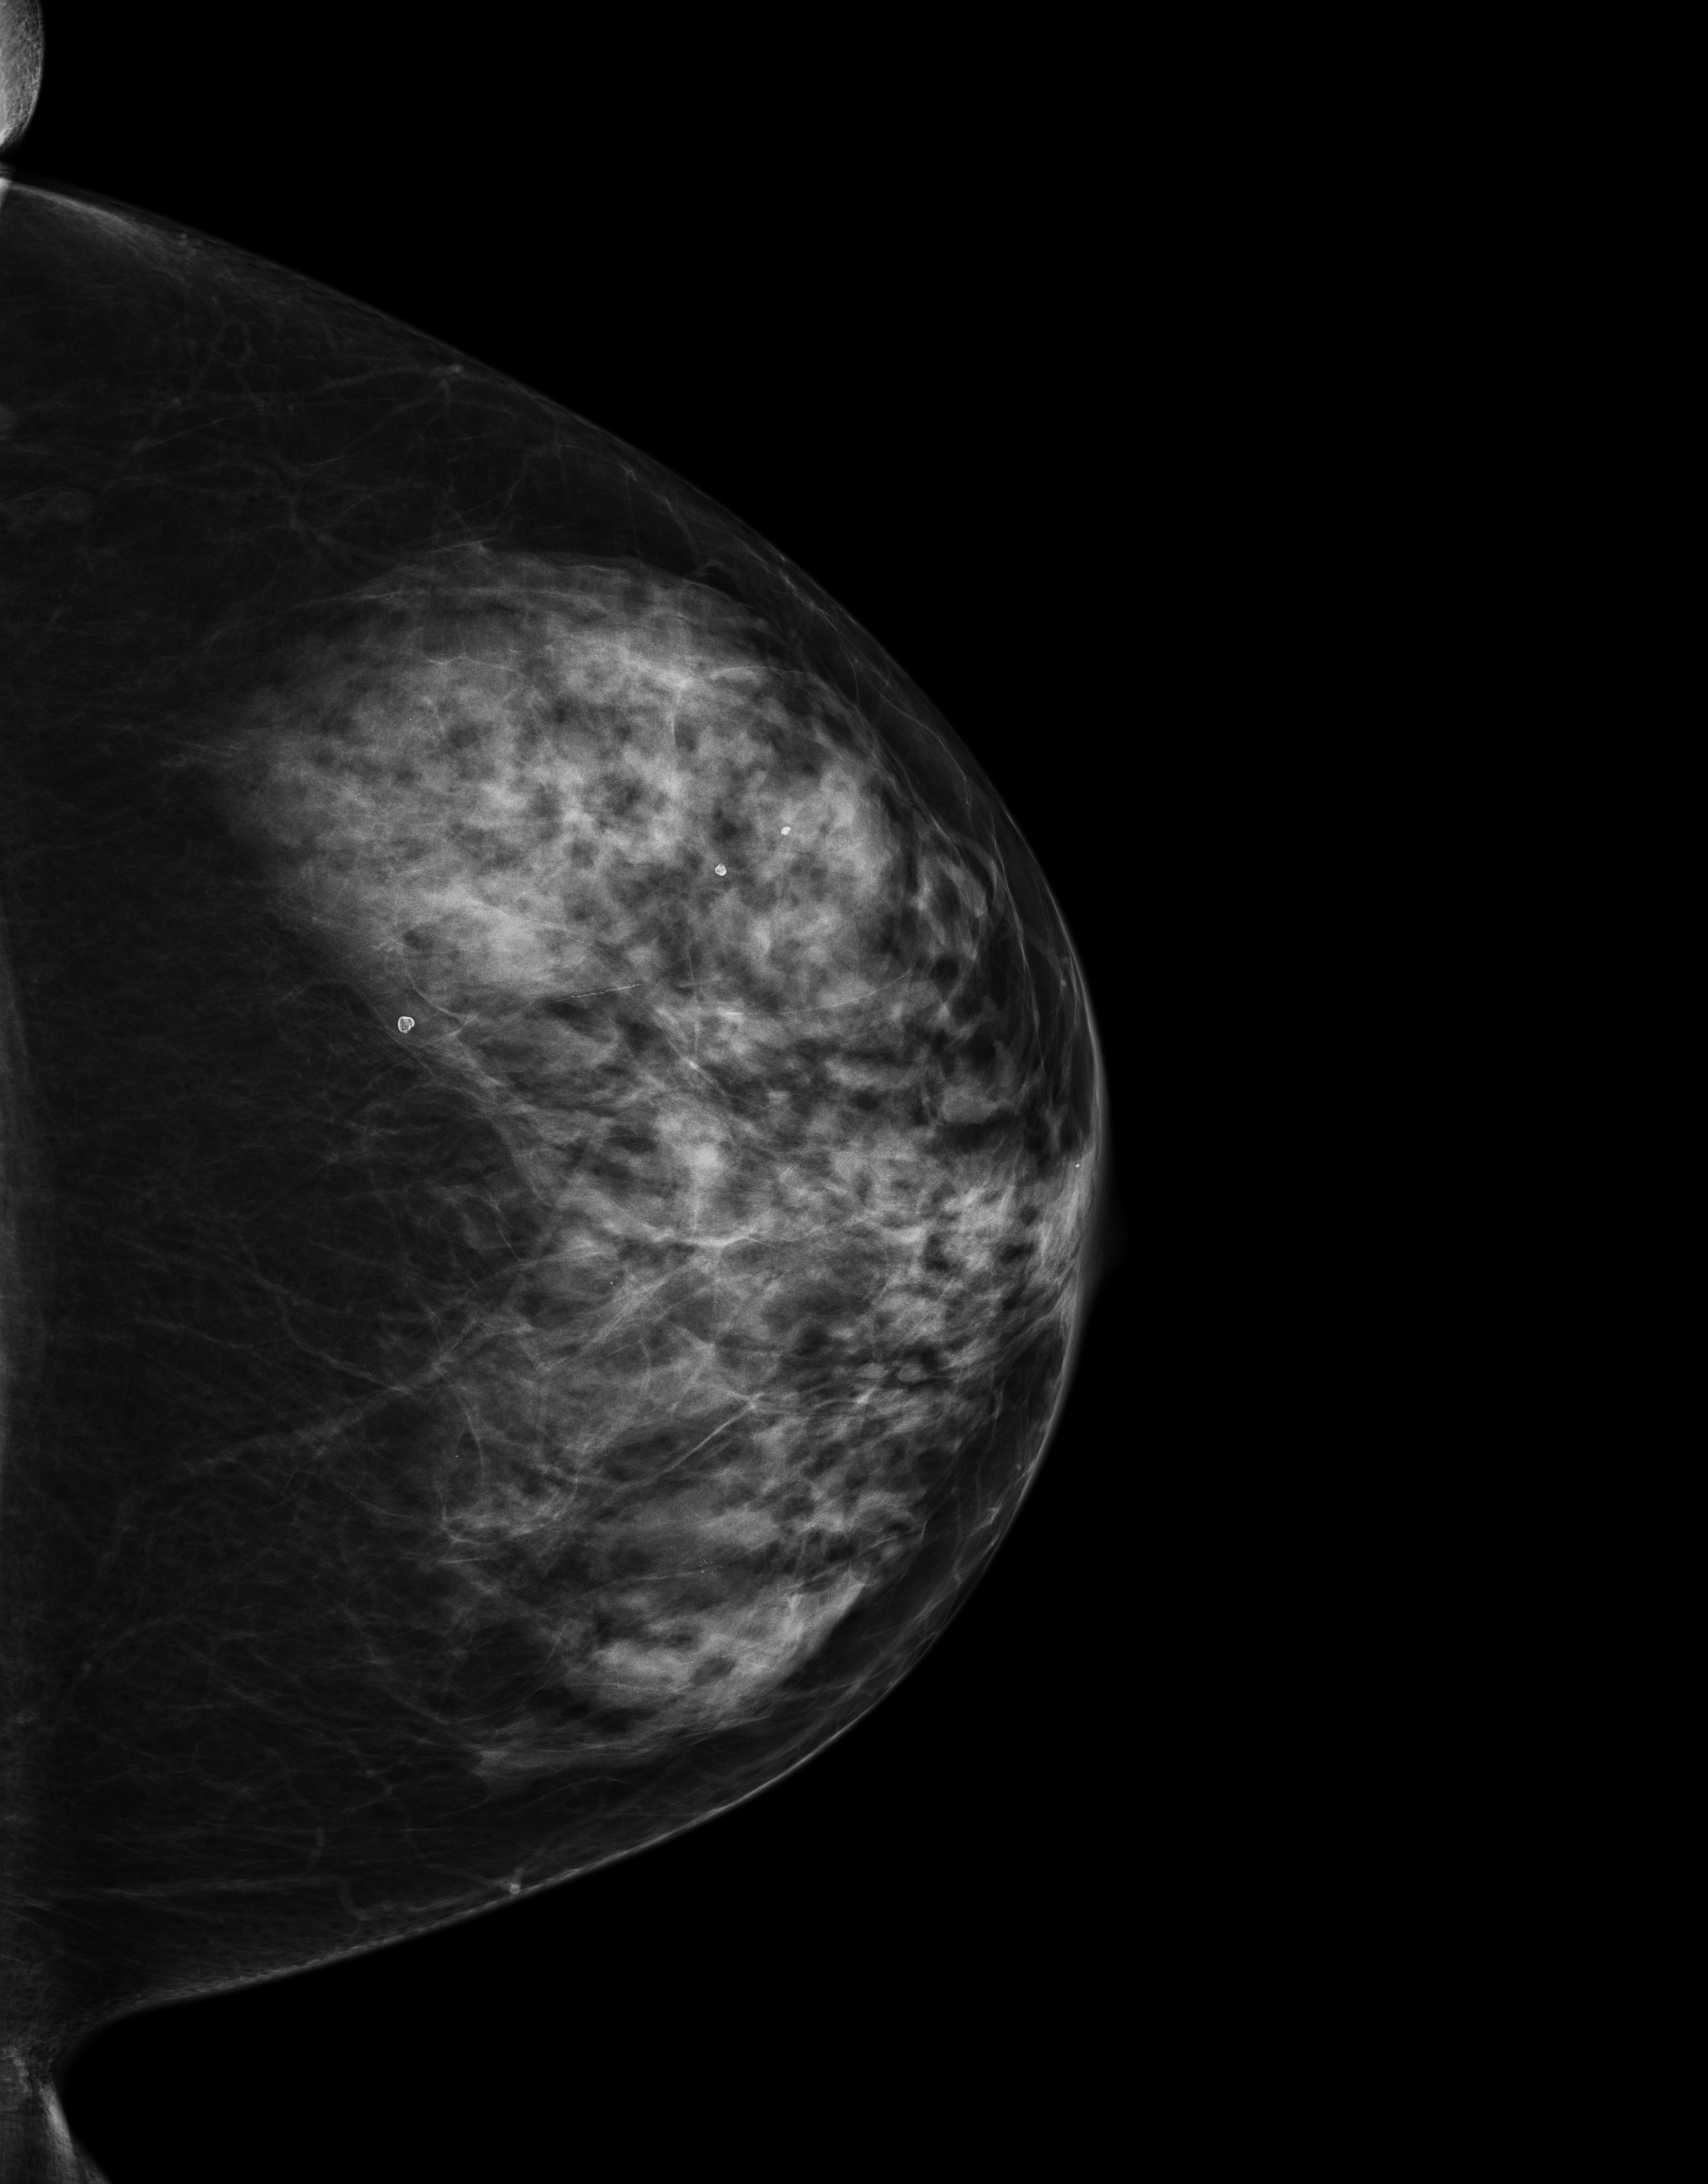
Digital mammogram (FFDM), left breast, cranio-caudal projection, annual screening mammography examination. Patient aged 65 years (female).
BI-RADS breast density category at the screening exam (both breasts, scale 1–4): 3.